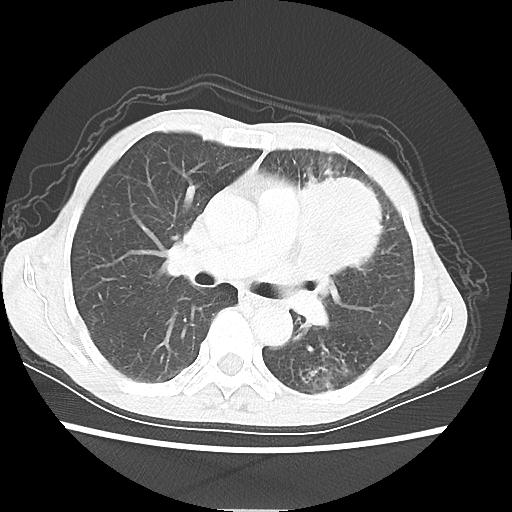
Chest CT, one axial slice. Position 35 of 56 along the scan axis. Reconstruction kernel LUNG. 80 kVp. Lung window (W 1500 / L -600 HU). 5 mm slice thickness. 512 × 512 image matrix. Female patient, age 60 years. From the clinical record (not read from this slice): clinical TNM (as recorded): T4 N1 M0.
Annotated regions visible in this slice (rectangle marked by the reading radiologist):
- lung tumour (recorded histology: adenocarcinoma): bounding box [x1, y1, x2, y2] px = [292, 163, 398, 279]